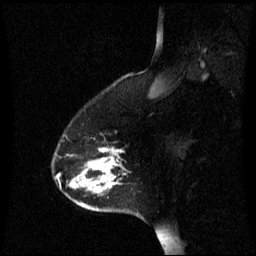
Breast MRI (dynamic contrast-enhanced), one sagittal slice; slice 14 of 60 in the series (ordered by position); dynamic contrast-enhanced series, image 2 of 3 at this slice position (ordered by acquisition); 1.5 T; TE 4.2 ms, TR 8.4 ms; 2.2 mm slice thickness; 256 × 256 image matrix, field of view 240 × 240 mm. Female patient, age 45 years. From the clinical record (not read from this slice): setting: breast cancer imaged before/during neoadjuvant chemotherapy; receptor status: HR-positive, HER2-negative.
Structures marked on this image (semi-automatic segmentation, software-assisted and operator-edited):
- analysis volume of interest (the breast-tissue region the enhancement analysis was run in; not a lesion): box from (x=52, y=144) to (x=137, y=215) px
- tumour enhancement mask (voxels above the 70 % enhancement threshold inside the analysis volume of interest): (x=72, y=148)–(x=121, y=191)